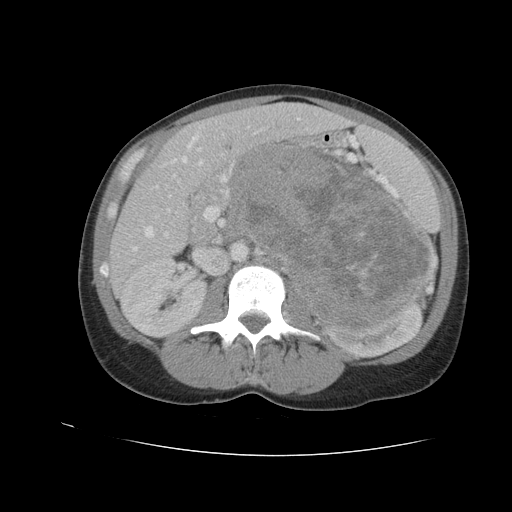
Contrast-enhanced abdominal CT, one axial slice. Slice 58 of 90 in the series (ordered by position). Reconstruction kernel STANDARD. 120 kVp. Intravenous contrast given. Soft-tissue window (W 400 / L 40 HU). 5 mm slice thickness. 512 × 512 image matrix, field of view 360 × 360 mm. Female patient. From the clinical record (not read from this slice): diagnosis: adrenocortical carcinoma; tumour side: left adrenal; tumour size at pathology: 18 cm; Ki-67 index: 11 %.
Annotated regions visible in this slice (semi-automatically segmented with operator editing):
- mass: bounding box <234,147,432,326> (left, top, right, bottom; pixels)